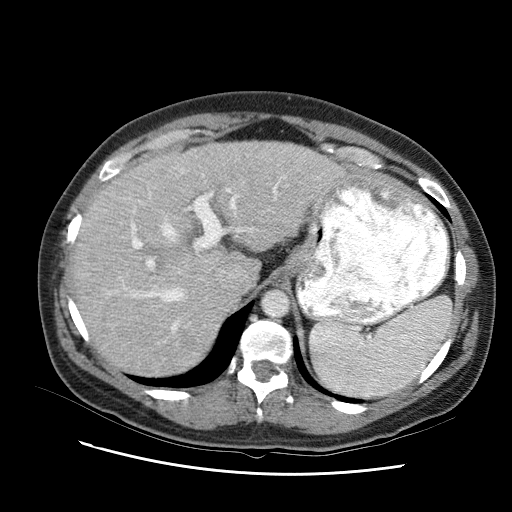
Contrast-enhanced abdominal CT (liver protocol), one axial slice; position 69 of 95 along the scan axis; reconstruction kernel STANDARD; 120 kVp; one of 2 acquisitions stored at this slice position; soft-tissue window (W 400 / L 40 HU); 2.5 mm slice thickness; 512 × 512 image matrix. Case-level facts recorded for this patient, not image findings: diagnosis: hepatocellular carcinoma (patient treated with transarterial chemoembolisation; whether this scan precedes or follows treatment is not stated here); TNM stage (as recorded): Stage-I; Child-Pugh class: B; tumour differentiation: moderately differentiated.
Outlined on this slice (semi-automatic segmentation, software-assisted and operator-edited):
- liver parenchyma outside the tumour (the mass and vessels are separate outlines, so this box may not span the whole liver): box from (x=70, y=138) to (x=344, y=362) px
- liver vessels: (x=104, y=181)–(x=275, y=331)